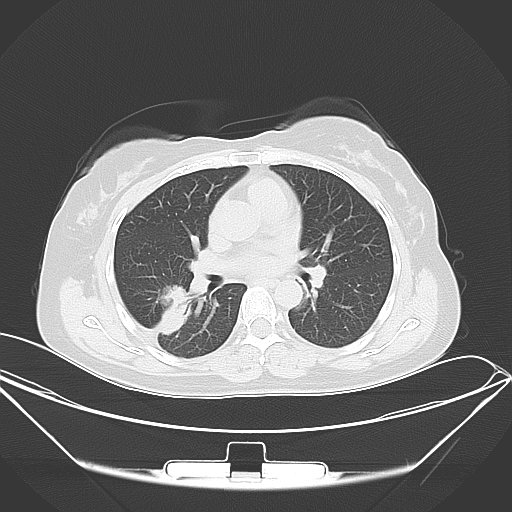
Chest CT, one axial slice; slice 22 of 46 in the series (ordered by position); lung window (W 1500 / L -600 HU); 512 × 512 image matrix, field of view 407 × 407 mm. Patient: female, 42 years. From the clinical record (not read from this slice): clinical TNM (as recorded): T1c N0 M1a.
Outlined on this slice (rectangle marked by the reading radiologist):
- lung tumour (recorded histology: adenocarcinoma): bounding box <148,279,194,339> (left, top, right, bottom; pixels)